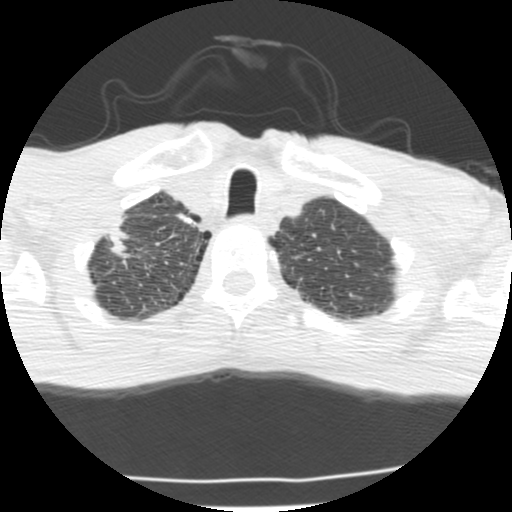
Chest CT (low-dose screening protocol), one axial image. Second annual screen. Lung window (W 1500 / L -600 HU). 120 kVp. 512 × 512 image matrix. Male, age 62 years at enrolment. Current smoker at enrolment.
Lesion marked by an expert reader, bounding box (x1, y1, x2, y2) in pixels: (81, 211, 146, 275). Screening reader's record for this exam (one nodule recorded; not confirmed to be the boxed lesion): non-calcified nodule or mass ≥4 mm, right upper lobe, 23 × 11 mm, spiculated (stellate) margins, soft tissue attenuation, pre-existing on the prior screen: yes. Official screen result: positive, change unspecified: nodule(s) >= 4 mm or enlarging nodule(s), mass(es), or other non-specific abnormalities suspicious for lung cancer. Lung cancer was diagnosed 277 days after this screen: adenocarcinoma, NOS, right upper lobe, poorly differentiated (G3), stage IIA (AJCC 6th edition), 22 mm at pathology.